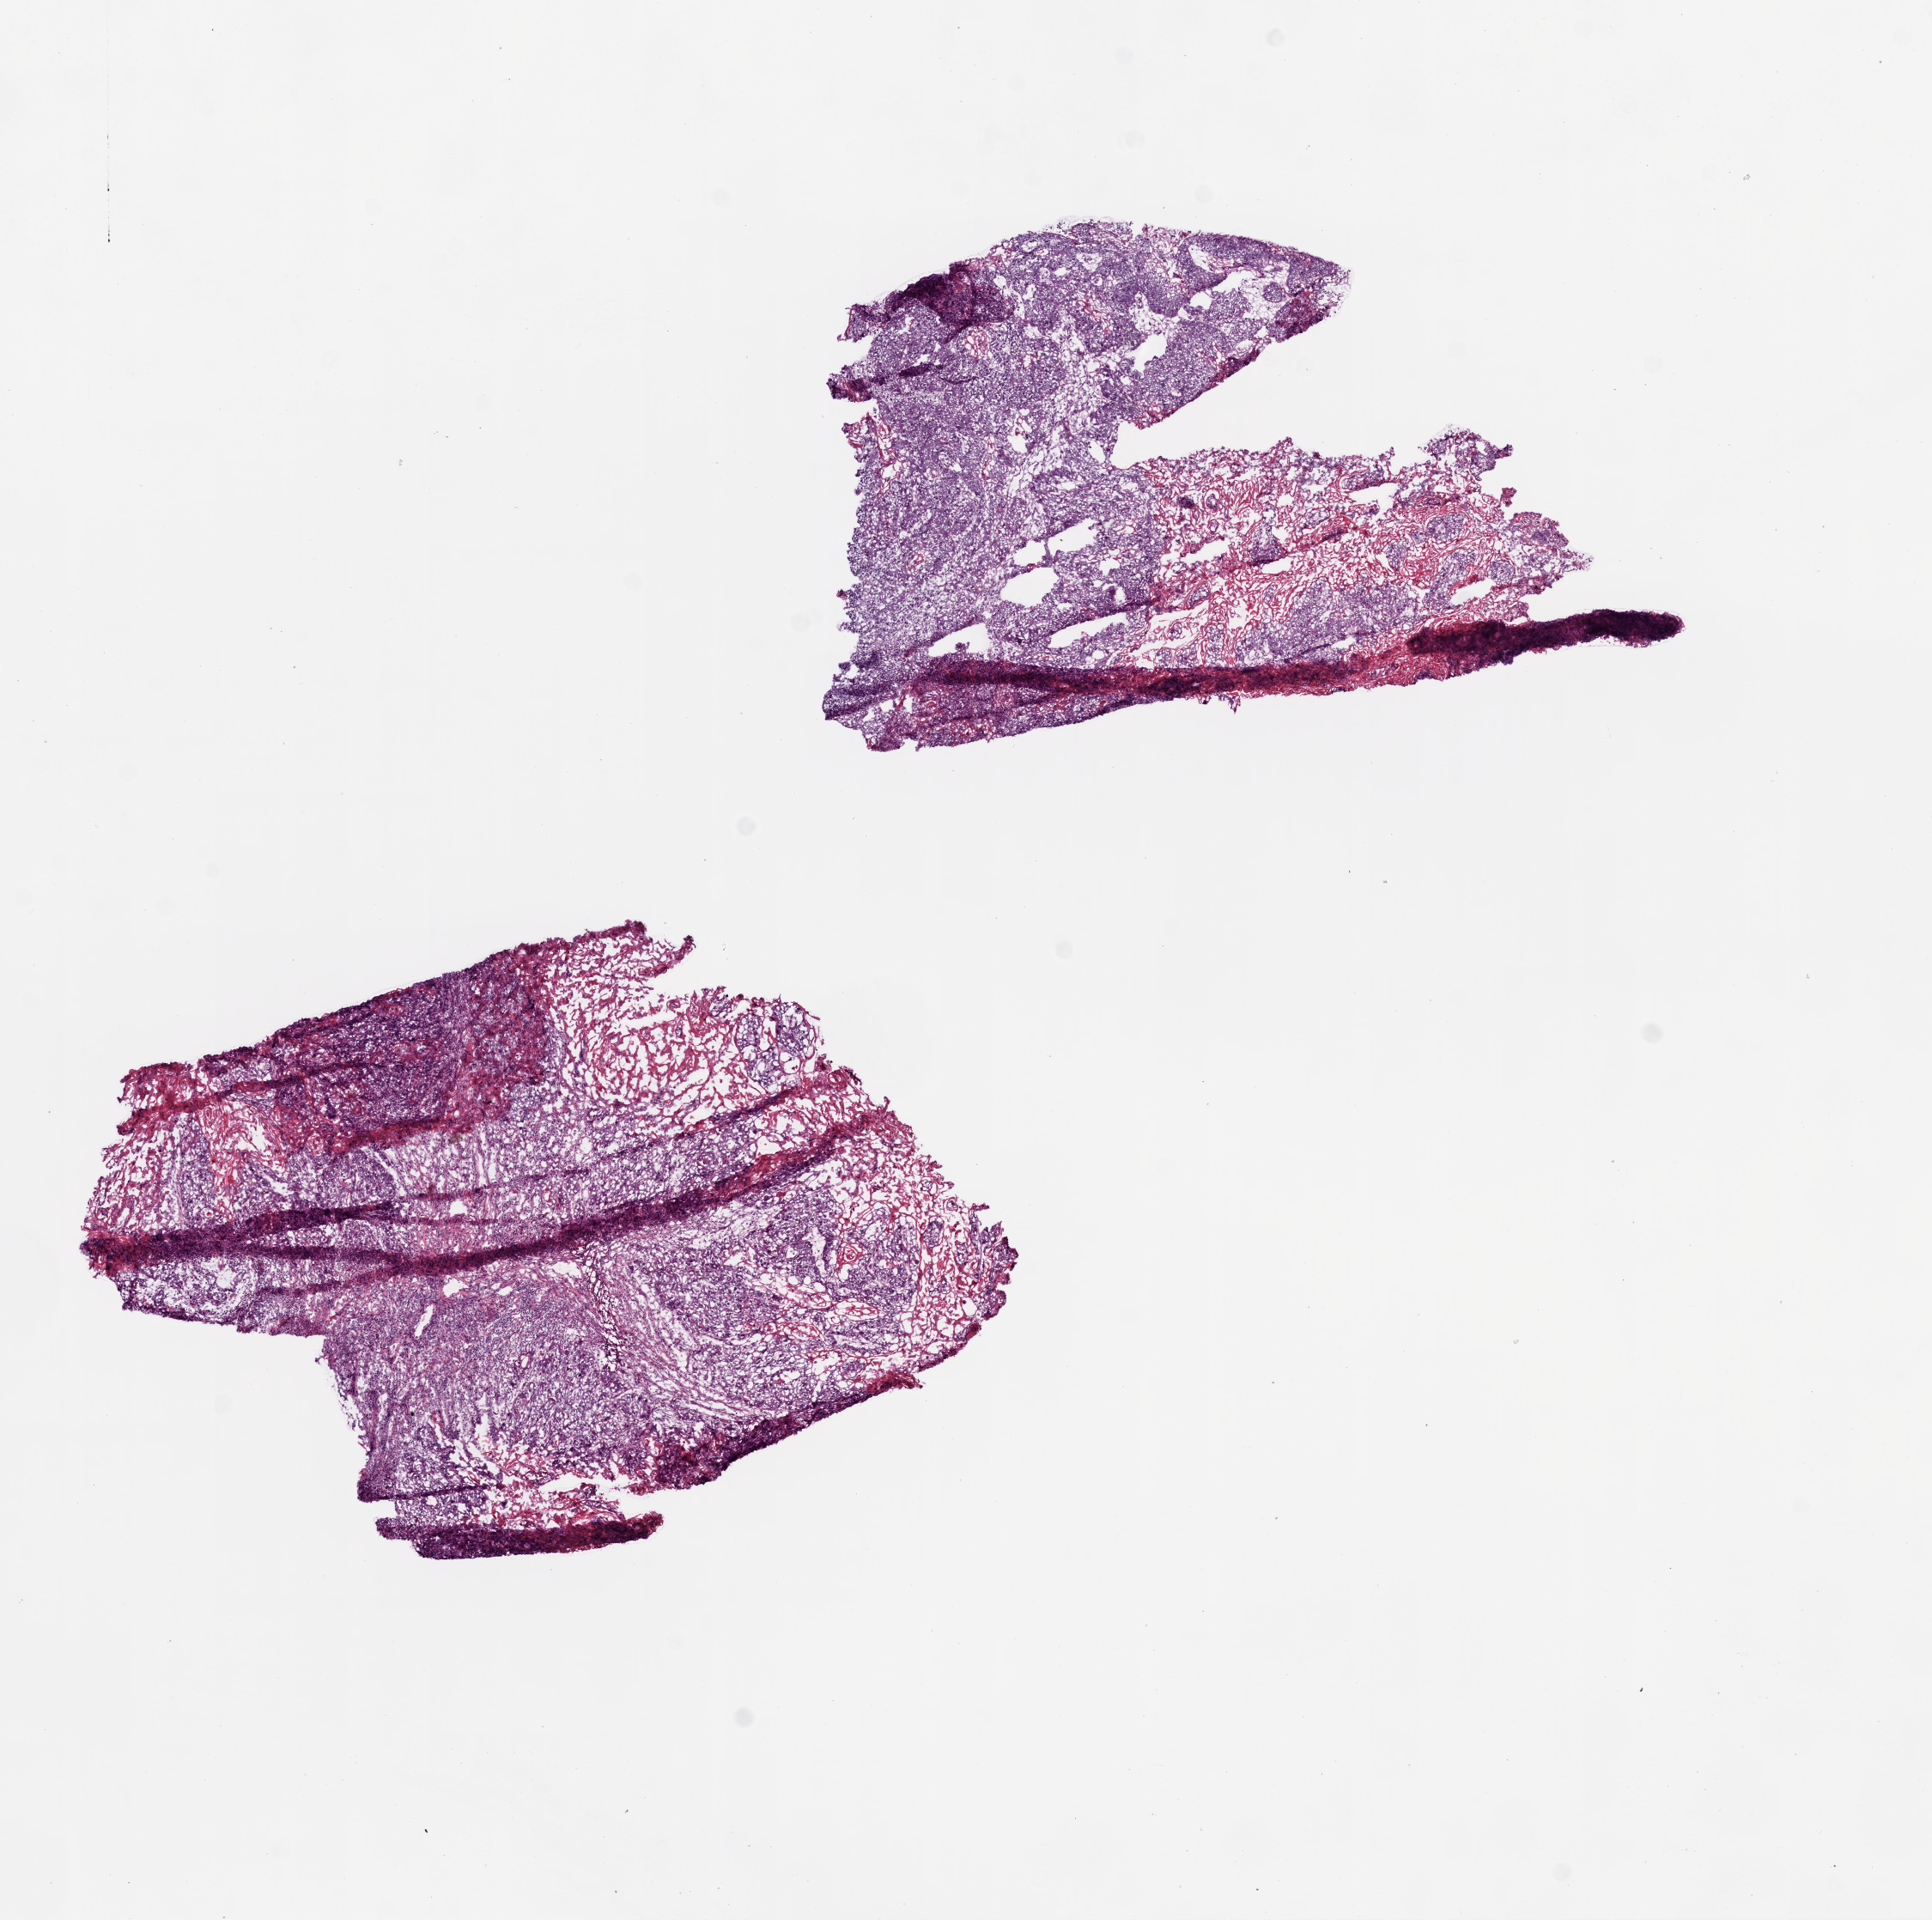
Whole-slide histology image, Hematoxylin and eosin (H&E) stained — a low-resolution overview of the entire scanned area, about 9.0 x 9.0 mm (slide scanned at 20x); frozen section from the top of the tissue portion; primary tumour sample from the head and neck. Male patient; age at initial diagnosis 62 years. Histologic grade: G2 (moderately differentiated). Composition of this section per pathologist review: tumour cells 85%, tumour nuclei 80%, normal cells 0%, stromal cells 15%, necrosis 0%.
- AJCC pathologic stage: IVA (7th edition)
- diagnosis: Squamous cell carcinoma, NOS (overlapping lesion of lip, oral cavity and pharynx)